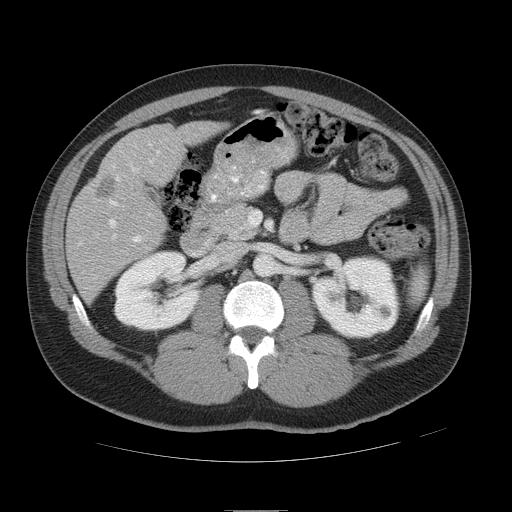
Contrast-enhanced abdominal CT, one axial slice. Position 22 of 49 along the scan axis. Reconstruction kernel STANDARD. 120 kVp. Intravenous contrast given. Soft-tissue window (W 400 / L 40 HU). 512 × 512 image matrix. Male patient, age 52 years. Case-level facts recorded for this patient, not image findings: diagnosis: colorectal cancer liver metastases, imaged before liver resection; multiple liver metastases: yes; largest metastasis: 5.1 cm; chemotherapy before resection: yes.
Structures marked on this image (outlined manually by an expert reader):
- hepatic veins: bounding box (x1, y1, x2, y2) in pixels: (109, 143, 152, 228)
- liver: (69, 124, 221, 299)
- planned liver remnant (the part of the liver to remain after resection): (133, 124, 221, 174)
- portal vein (with intrahepatic branches): (98, 164, 151, 243)
- liver metastasis: (96, 176, 118, 201)